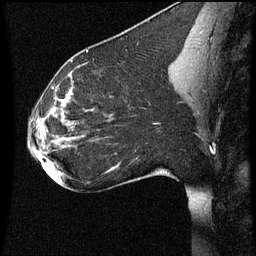
Breast MRI (dynamic contrast-enhanced), one sagittal slice; slice 30 of 60 in the series (ordered by position); dynamic contrast-enhanced series, image 2 of 3 at this slice position (ordered by acquisition); 1.5 T; TE 4.2 ms, TR 8.9 ms; 256 × 256 image matrix. Female patient, age 35 years. From the clinical record (not read from this slice): setting: breast cancer imaged before/during neoadjuvant chemotherapy; receptor status: HER2-positive.
Structures marked on this image (semi-automatic segmentation, software-assisted and operator-edited):
- analysis volume of interest (the breast-tissue region the enhancement analysis was run in; not a lesion): bounding box <26,66,177,177> (left, top, right, bottom; pixels)
- tumour enhancement mask (voxels above the 70 % enhancement threshold inside the analysis volume of interest): <54,94,72,141>